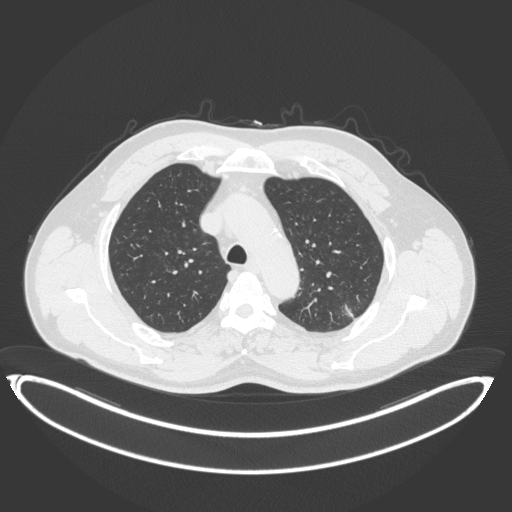
Chest CT, one axial slice. Slice 275 of 399 in the series (ordered by position). Reconstruction kernel B31f. 120 kVp. Lung window (W 1500 / L -600 HU). 512 × 512 image matrix, field of view 469 × 469 mm. Male patient, age 58 years. Case-level facts recorded for this patient, not image findings: clinical TNM (as recorded): T1c N0 M0.
Outlined on this slice (bounding box drawn by a radiologist):
- lung tumour (recorded histology: adenocarcinoma): bounding box (x1, y1, x2, y2) in pixels: (340, 300, 363, 322)